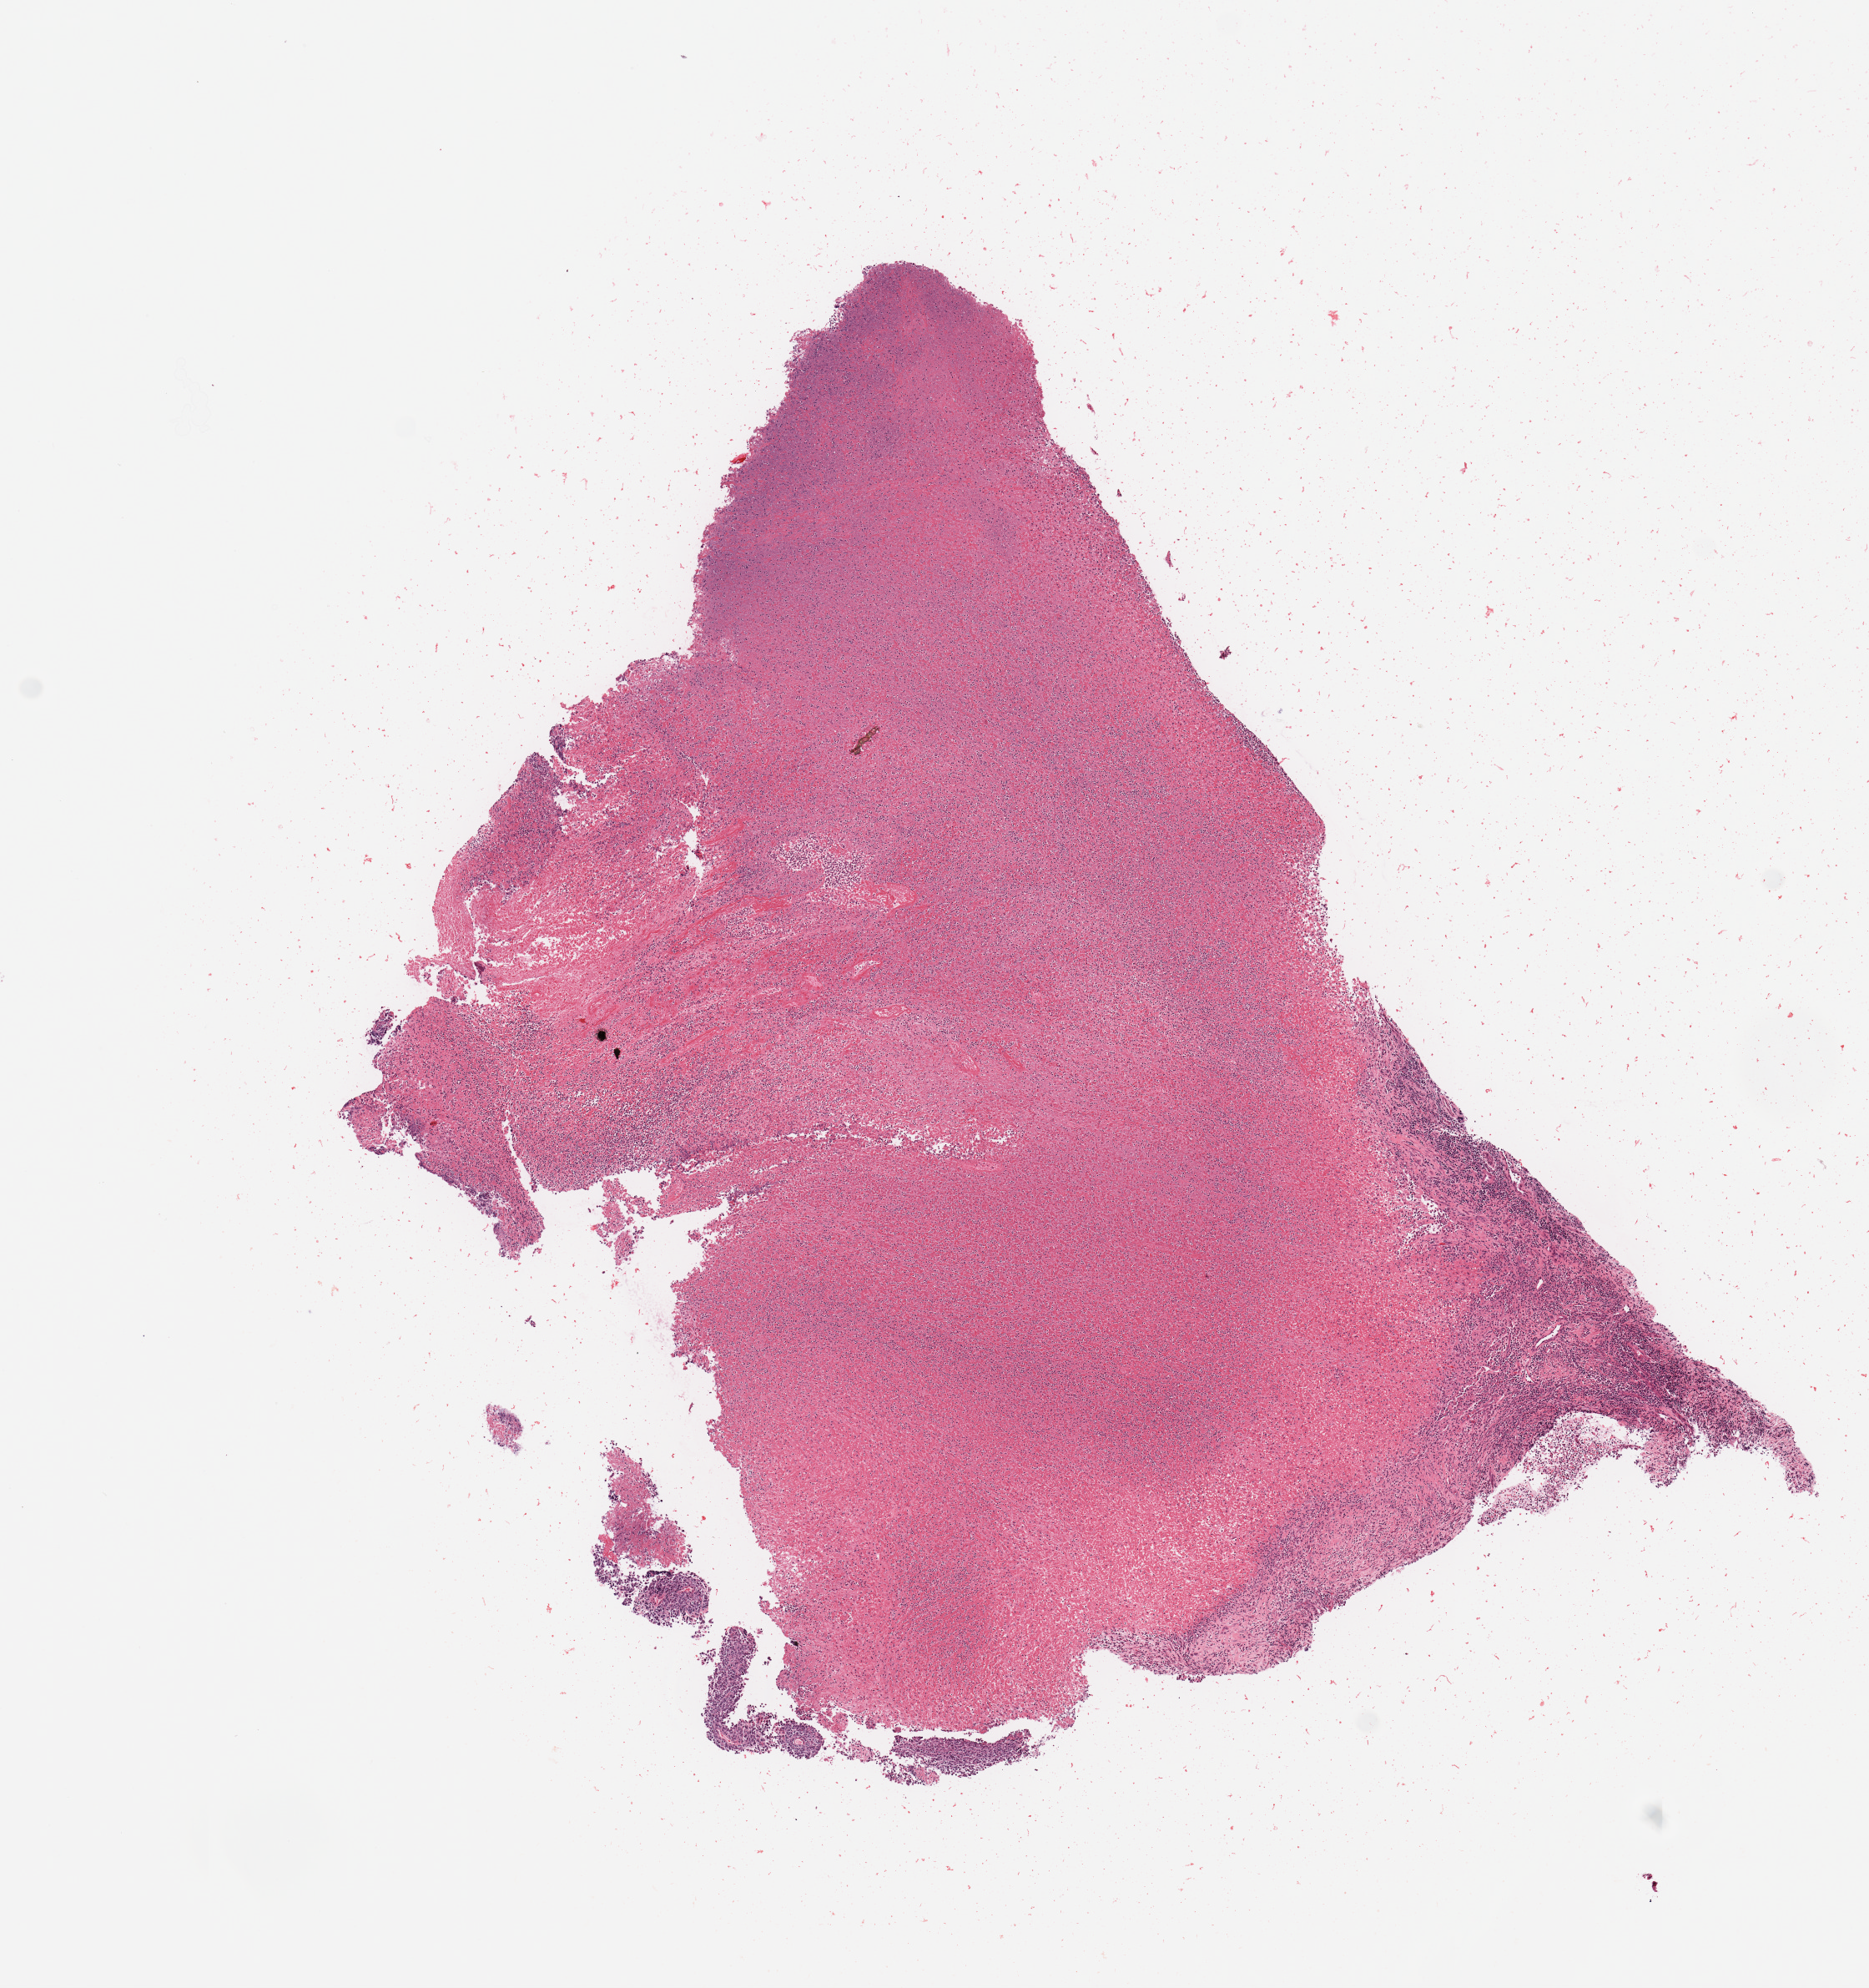
Hematoxylin and eosin (H&E) stained whole-slide image, whole scanned area (about 8.9 x 9.4 mm, from a 20x scan) shown as a low-resolution overview, tumour tissue sample, uterus. 51-year-old female patient. Histologic grade: G3 (poorly differentiated).
- histologic diagnosis: Endometrioid adenocarcinoma, NOS